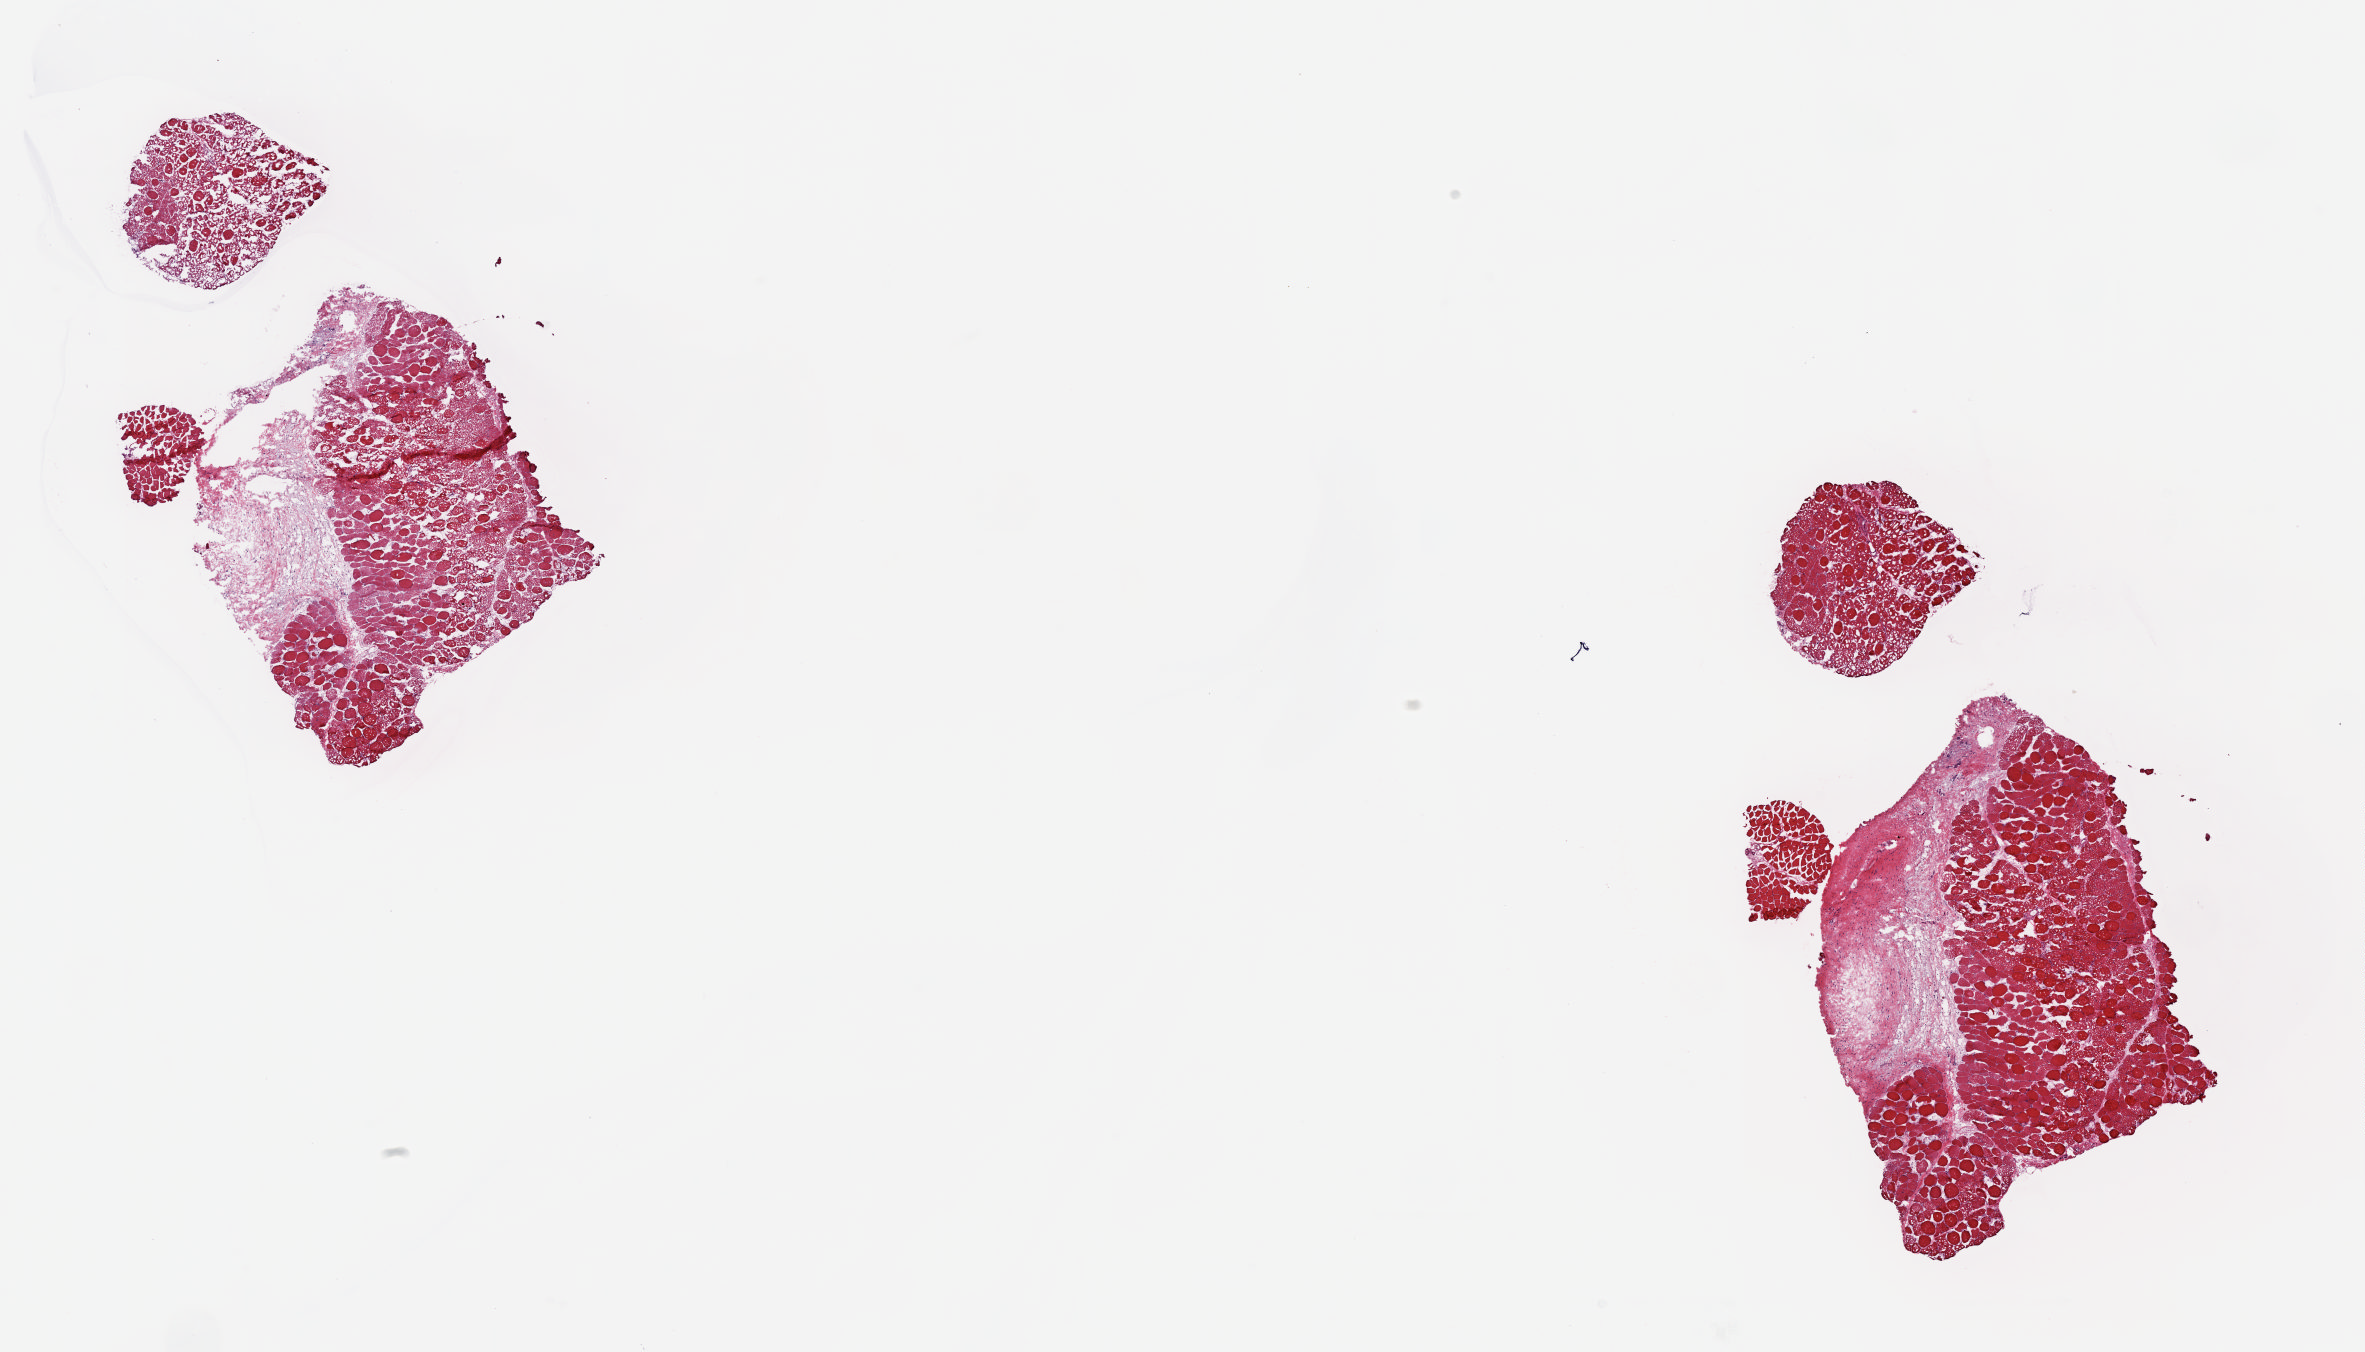
Digitized H&E-stained tissue section (whole slide) — a low-resolution overview of the entire scanned area, about 18.7 x 10.7 mm. Frozen section. Breast, solid tissue normal (non-tumour tissue) sample. Patient: female, age at initial diagnosis 63 years. Composition of this section per pathologist review: tumour cells 0%, tumour nuclei 0%, normal cells 0%, stromal cells 100%, necrosis 0%. Infiltration values recorded for this section: lymphocyte infiltration 0%, monocyte infiltration 0%, neutrophil infiltration 0%.
- this section: solid tissue normal sample (biorepository sample class)
- patient diagnosis: Infiltrating duct carcinoma, NOS